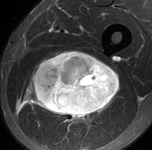
MRI of an extremity soft-tissue mass, one axial slice; position 67 of 90 along the scan axis; STIR; MR volume resampled by the dataset authors to the PET/CT grid (not the native acquisition matrix); 152 × 150 image matrix. Male patient. From the clinical record (not read from this slice): histological type: undifferentiated pleomorphic liposarcoma; grade: high; site of the primary tumour: left thigh.
Structures marked on this image (expert contour drawn on MRI and transferred to this co-registered scan by the dataset authors):
- gross tumour volume including surrounding oedema: bounding box (x1, y1, x2, y2) in pixels: (20, 50, 119, 127)
- gross tumour volume (mass): (27, 50, 119, 117)